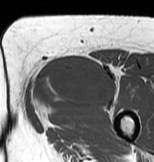
MRI of an extremity soft-tissue mass, one axial slice; MR volume resampled by the dataset authors to the PET/CT grid (not the native acquisition matrix); 3.27 mm slice thickness; 154 × 162 image matrix, field of view 150 × 158 mm. Female patient. From the clinical record (not read from this slice): histological type: myxofibrosarcoma; grade: intermediate; site of the primary tumour: left thigh.
Outlined on this slice (expert contour drawn on MRI and transferred to this co-registered scan by the dataset authors):
- gross tumour volume including surrounding oedema: bounding box <28,52,120,124> (left, top, right, bottom; pixels)
- gross tumour volume (mass): <31,52,114,108>